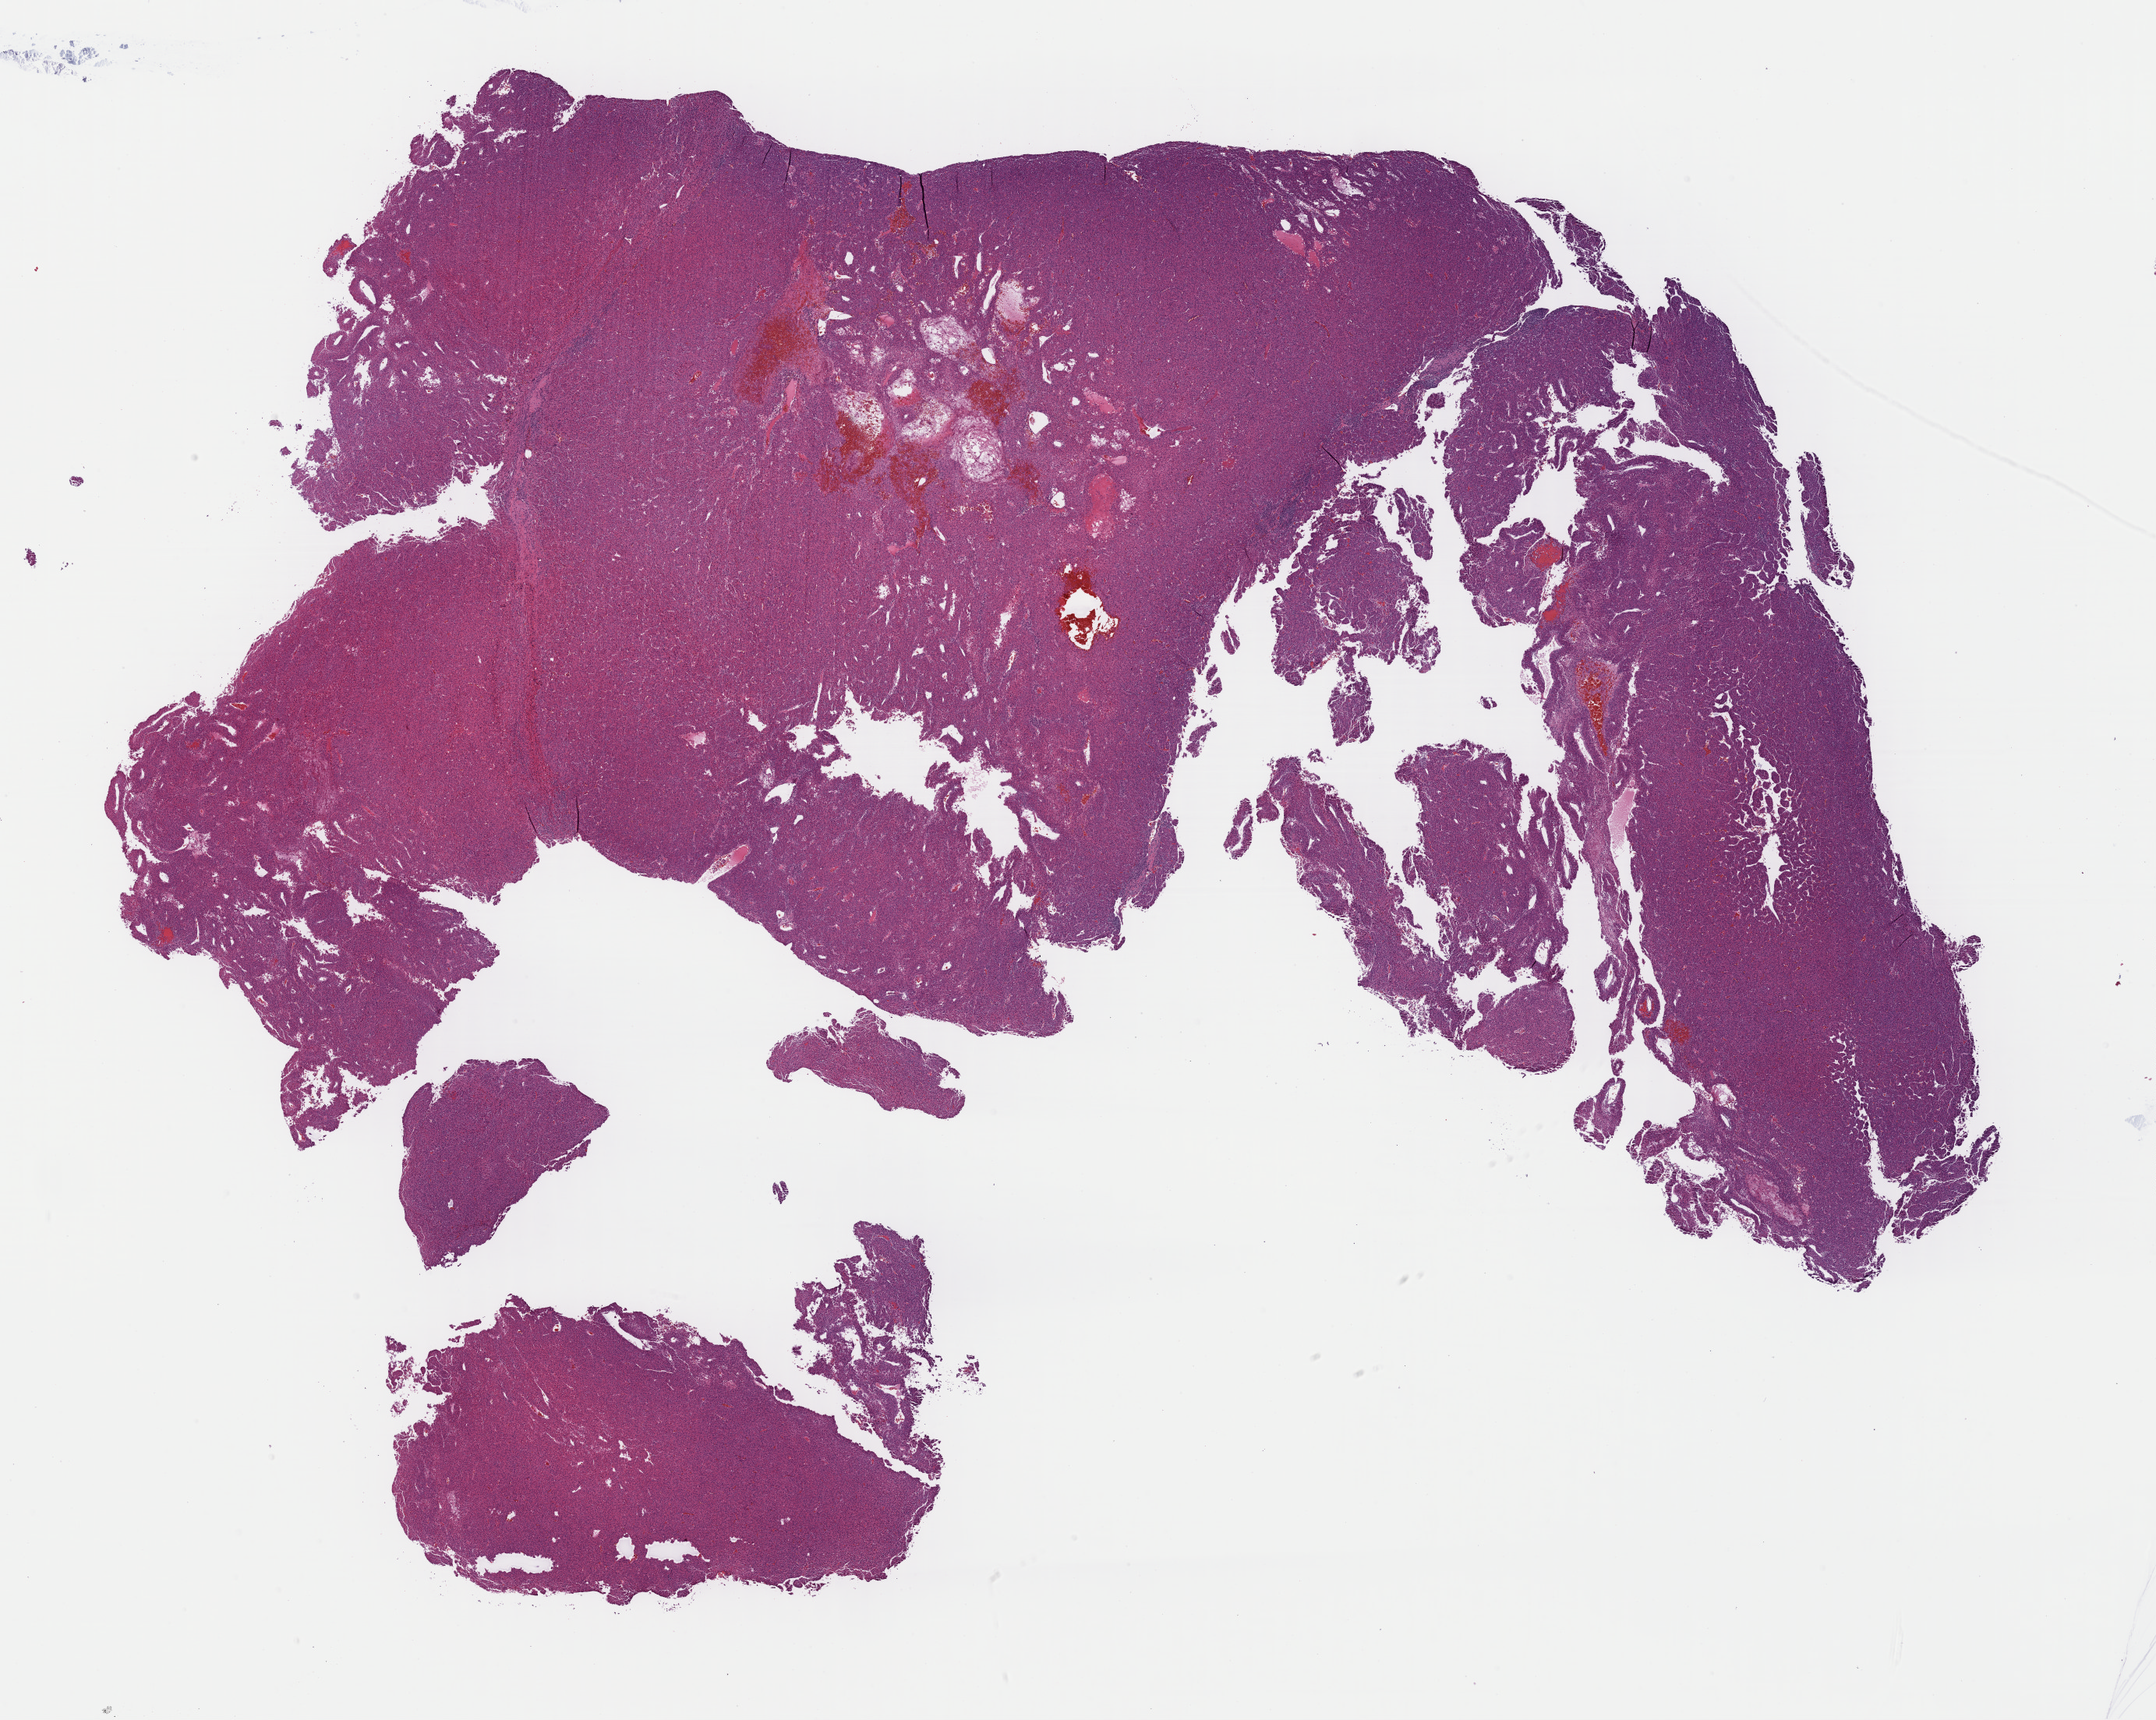
Digitized H&E tissue section (whole slide), a low-resolution overview of the entire scanned area, about 21.9 x 17.4 mm; formalin-fixed paraffin-embedded (FFPE) diagnostic section; primary tumour sample from the liver. Patient: male, age at initial diagnosis 73 years. Histologic grade: G2 (moderately differentiated).
* AJCC pathologic stage: IIIA (7th edition)
* pathologic diagnosis: Hepatocellular carcinoma, NOS
* TNM: T3a NX MX